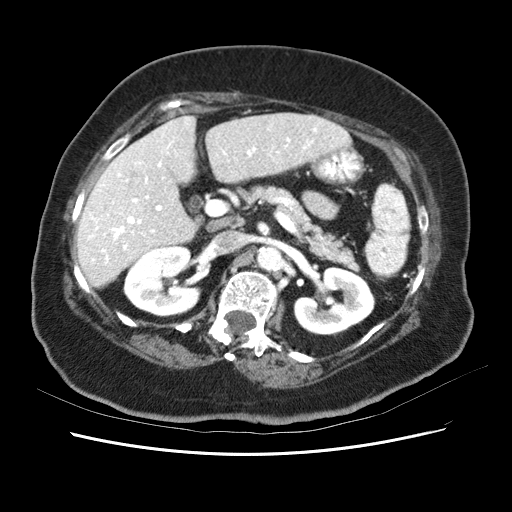
Contrast-enhanced abdominal CT (liver protocol), one axial slice; position 28 of 62 along the scan axis; soft-tissue window (W 400 / L 40 HU); 512 × 512 image matrix. Case-level facts recorded for this patient, not image findings: diagnosis: hepatocellular carcinoma (patient treated with transarterial chemoembolisation; whether this scan precedes or follows treatment is not stated here); TNM stage (as recorded): Stage-I; Child-Pugh class: B.
Annotated regions visible in this slice (semi-automatically segmented with operator editing):
- liver parenchyma outside the tumour (the mass and vessels are separate outlines, so this box may not span the whole liver): box from (x=76, y=112) to (x=355, y=288) px
- liver vessels: (x=79, y=125)–(x=353, y=271)